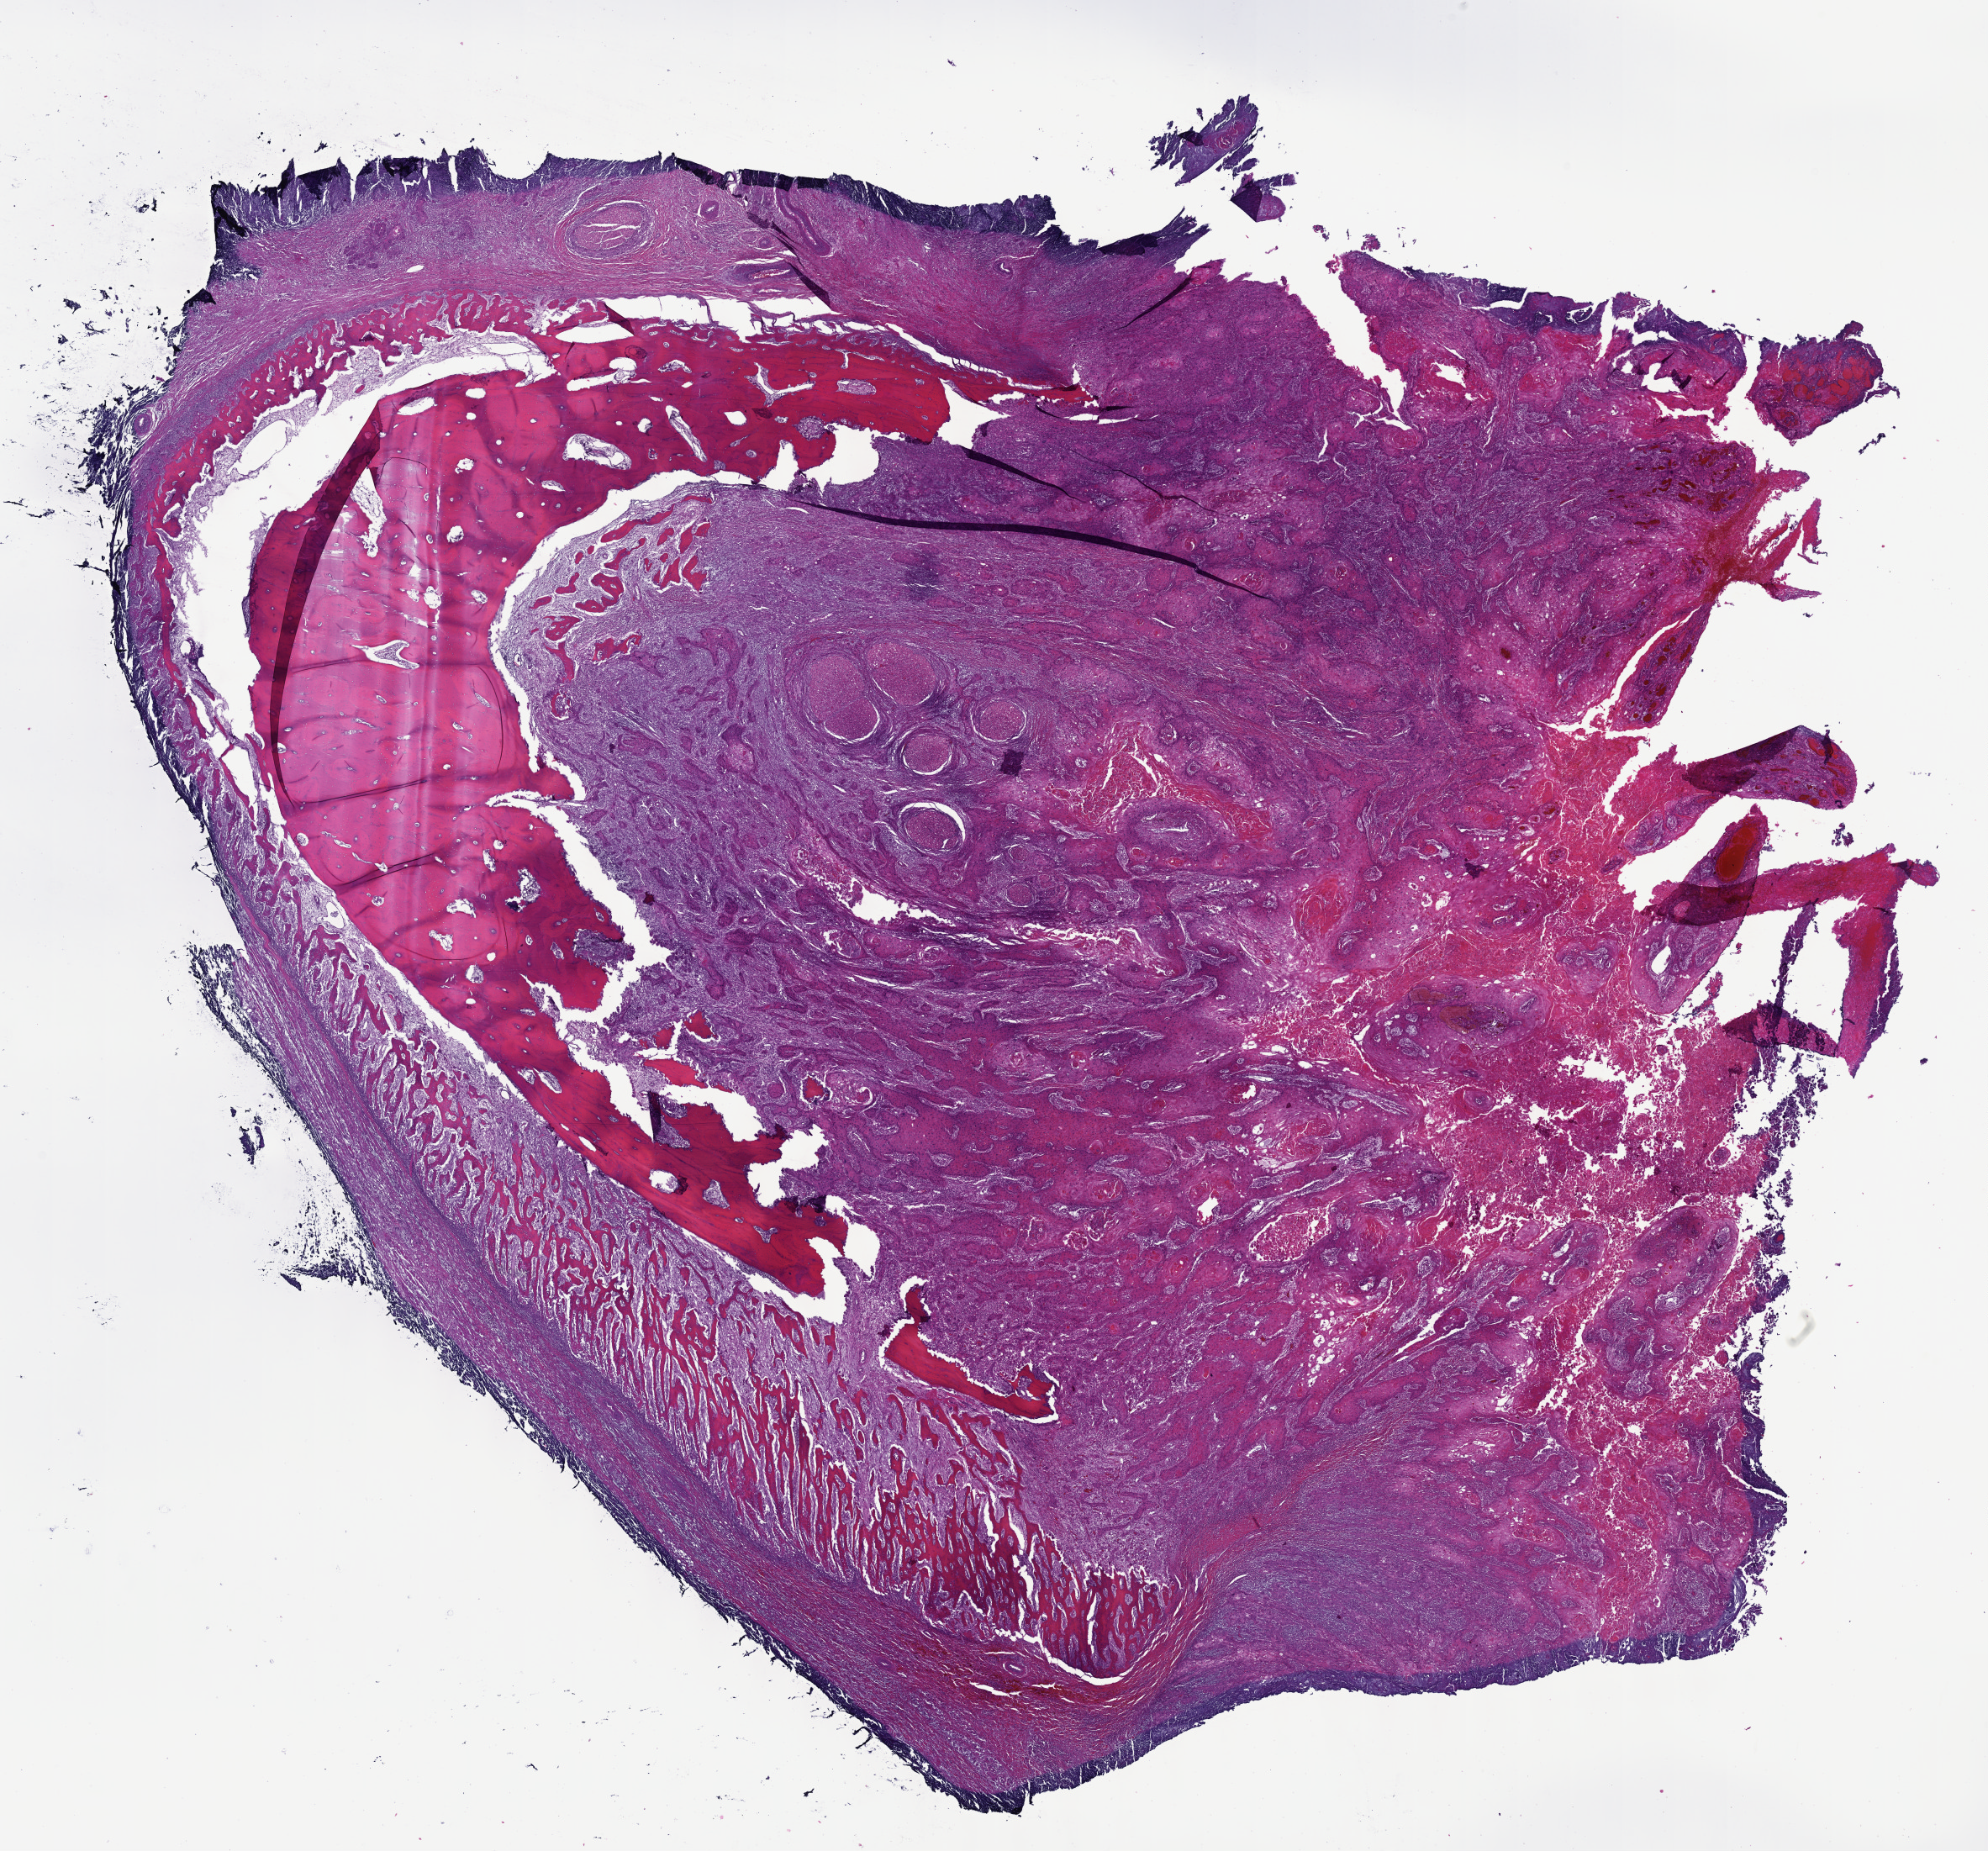
Hematoxylin and eosin (H&E) stained whole-slide image, low-resolution overview of the scanned area, about 19.1 x 17.8 mm (from a 40x scan). FFPE section. Sample: primary tumour, head and neck. Female patient; age at initial diagnosis 62 years. Histologic grade: G2 (moderately differentiated).
AJCC pathologic stage: IVA (7th edition). Histologic diagnosis: Squamous cell carcinoma, NOS (overlapping lesion of lip, oral cavity and pharynx). Lymph nodes positive (case pathology): 0 of 34 examined. TNM: T4a N0.